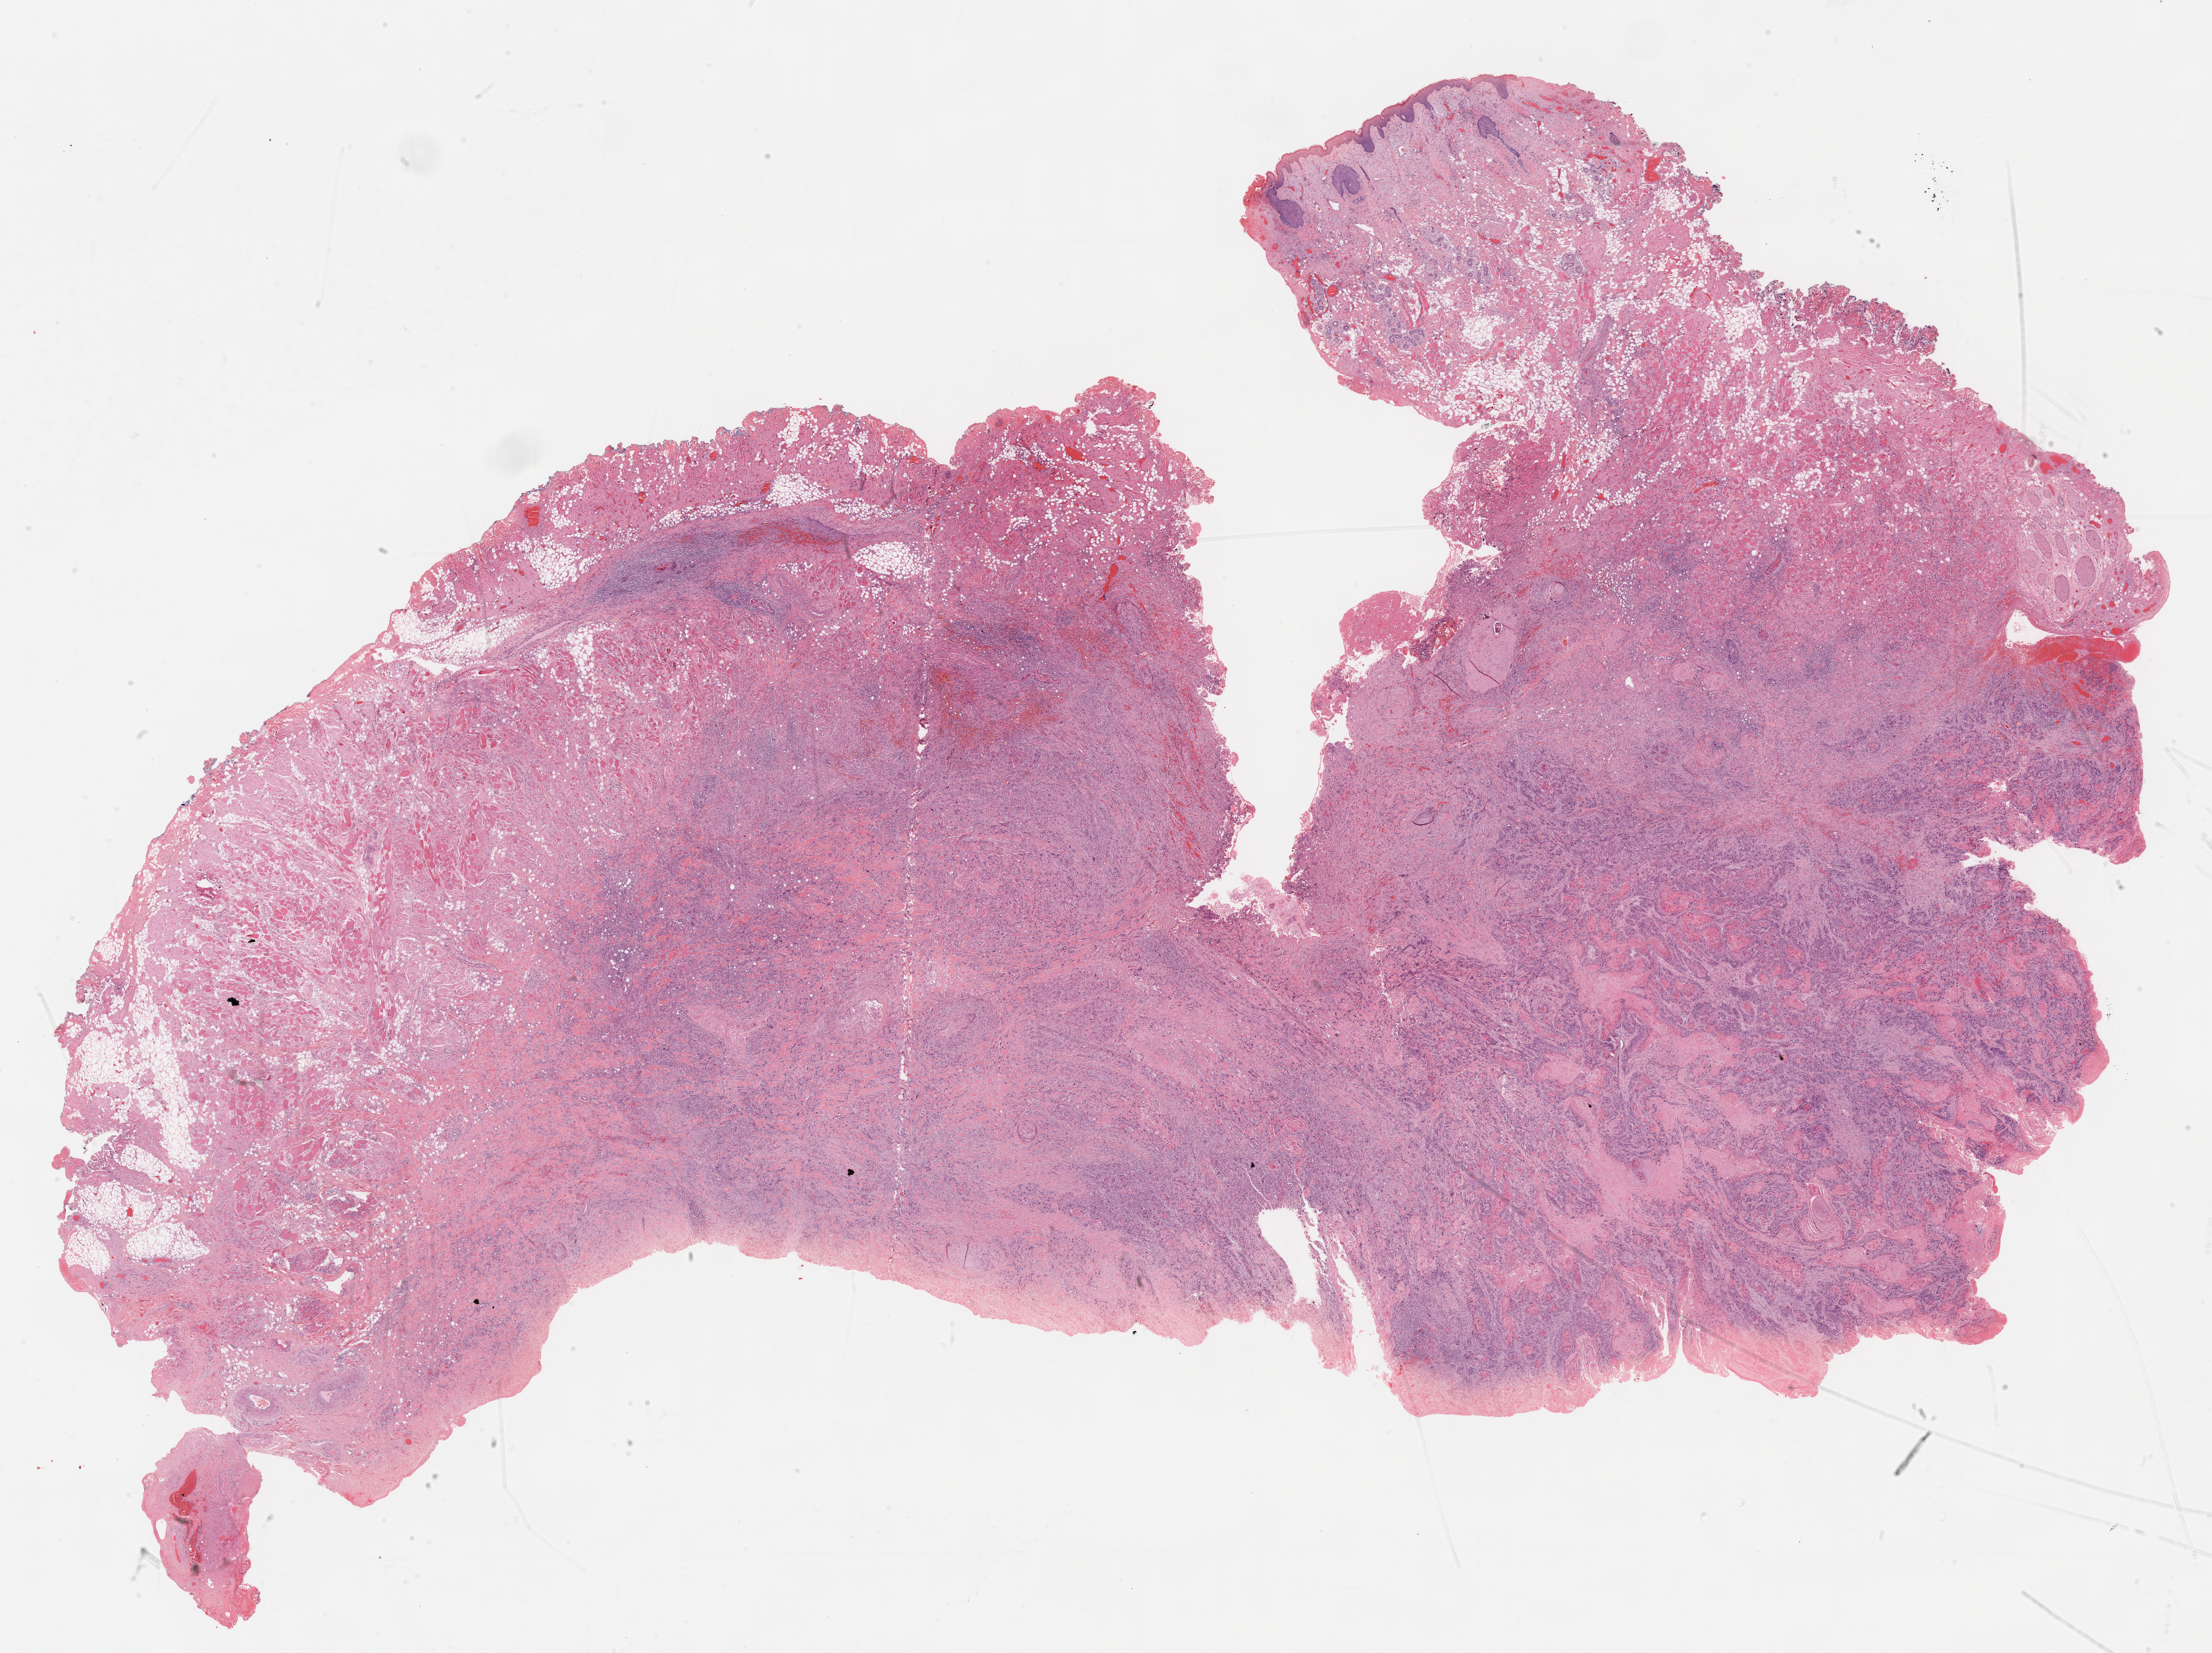
Hematoxylin and eosin (H&E) stained whole-slide image — low-resolution overview of the scanned area, about 27.2 x 20.3 mm, formalin-fixed paraffin-embedded (FFPE) diagnostic section, primary tumour sample from the head and neck. Male patient; age at initial diagnosis 53 years. Histologic grade: G3 (poorly differentiated).
• AJCC pathologic stage: II (7th edition)
• TNM: T2 NX
• pathologic diagnosis: Squamous cell carcinoma, NOS (overlapping lesion of lip, oral cavity and pharynx)